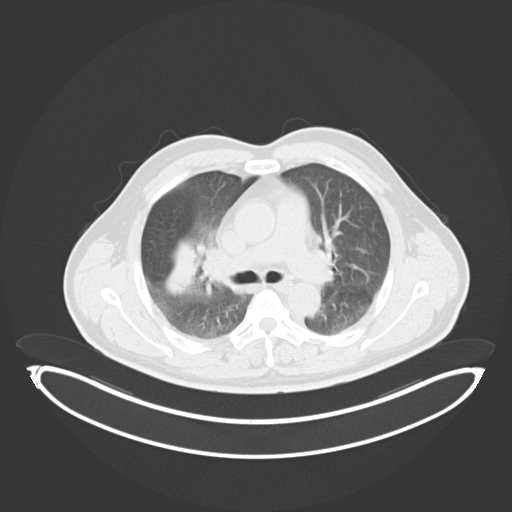
Chest CT, one axial slice; slice 214 of 284 in the series (ordered by position); 120 kVp; lung window (W 1500 / L -600 HU); 3 mm slice thickness; 512 × 512 image matrix, field of view 500 × 500 mm. Male patient, age 55 years. Case-level facts recorded for this patient, not image findings: clinical TNM (as recorded): T3 N2 M1.
Annotated regions visible in this slice (bounding box drawn by a radiologist):
- lung tumour (recorded histology: adenocarcinoma): bounding box <152,234,204,300> (left, top, right, bottom; pixels)